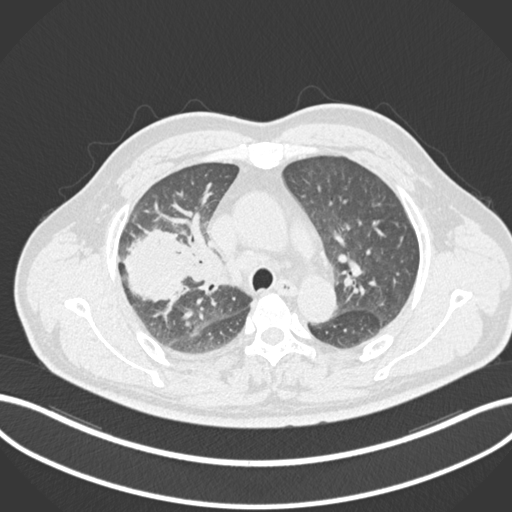
Chest CT, one axial slice. Slice 659 of 852 in the series (ordered by position). Reconstruction kernel B30f. 120 kVp. Lung window (W 1500 / L -600 HU). 1 mm slice thickness. 512 × 512 image matrix, field of view 400 × 400 mm. Patient: male, 55 years. Case-level facts recorded for this patient, not image findings: clinical TNM (as recorded): T3 N2 M1.
Annotated regions visible in this slice (bounding box drawn by a radiologist):
- lung tumour (recorded histology: adenocarcinoma): bounding box [x1, y1, x2, y2] px = [119, 224, 197, 302]